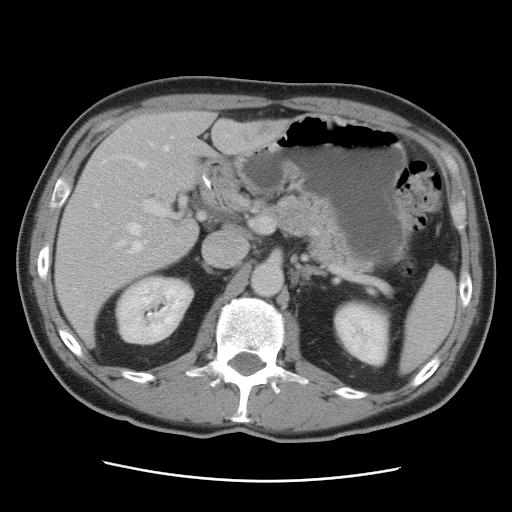
Contrast-enhanced abdominal CT, one axial slice. 120 kVp. Intravenous contrast given. Soft-tissue window (W 400 / L 40 HU). 512 × 512 image matrix, field of view 366 × 366 mm. Male patient, age 59 years. From the clinical record (not read from this slice): diagnosis: colorectal cancer liver metastases, imaged before liver resection; multiple liver metastases: yes; largest metastasis: 0.6 cm; disease in both lobes: yes.
Structures marked on this image (expert manual segmentation):
- hepatic veins: bounding box [x1, y1, x2, y2] px = [95, 136, 237, 254]
- liver: [54, 112, 289, 346]
- planned liver remnant (the part of the liver to remain after resection): [71, 112, 216, 243]
- portal vein (with intrahepatic branches): [143, 200, 263, 241]
- liver metastasis: [245, 124, 280, 141]